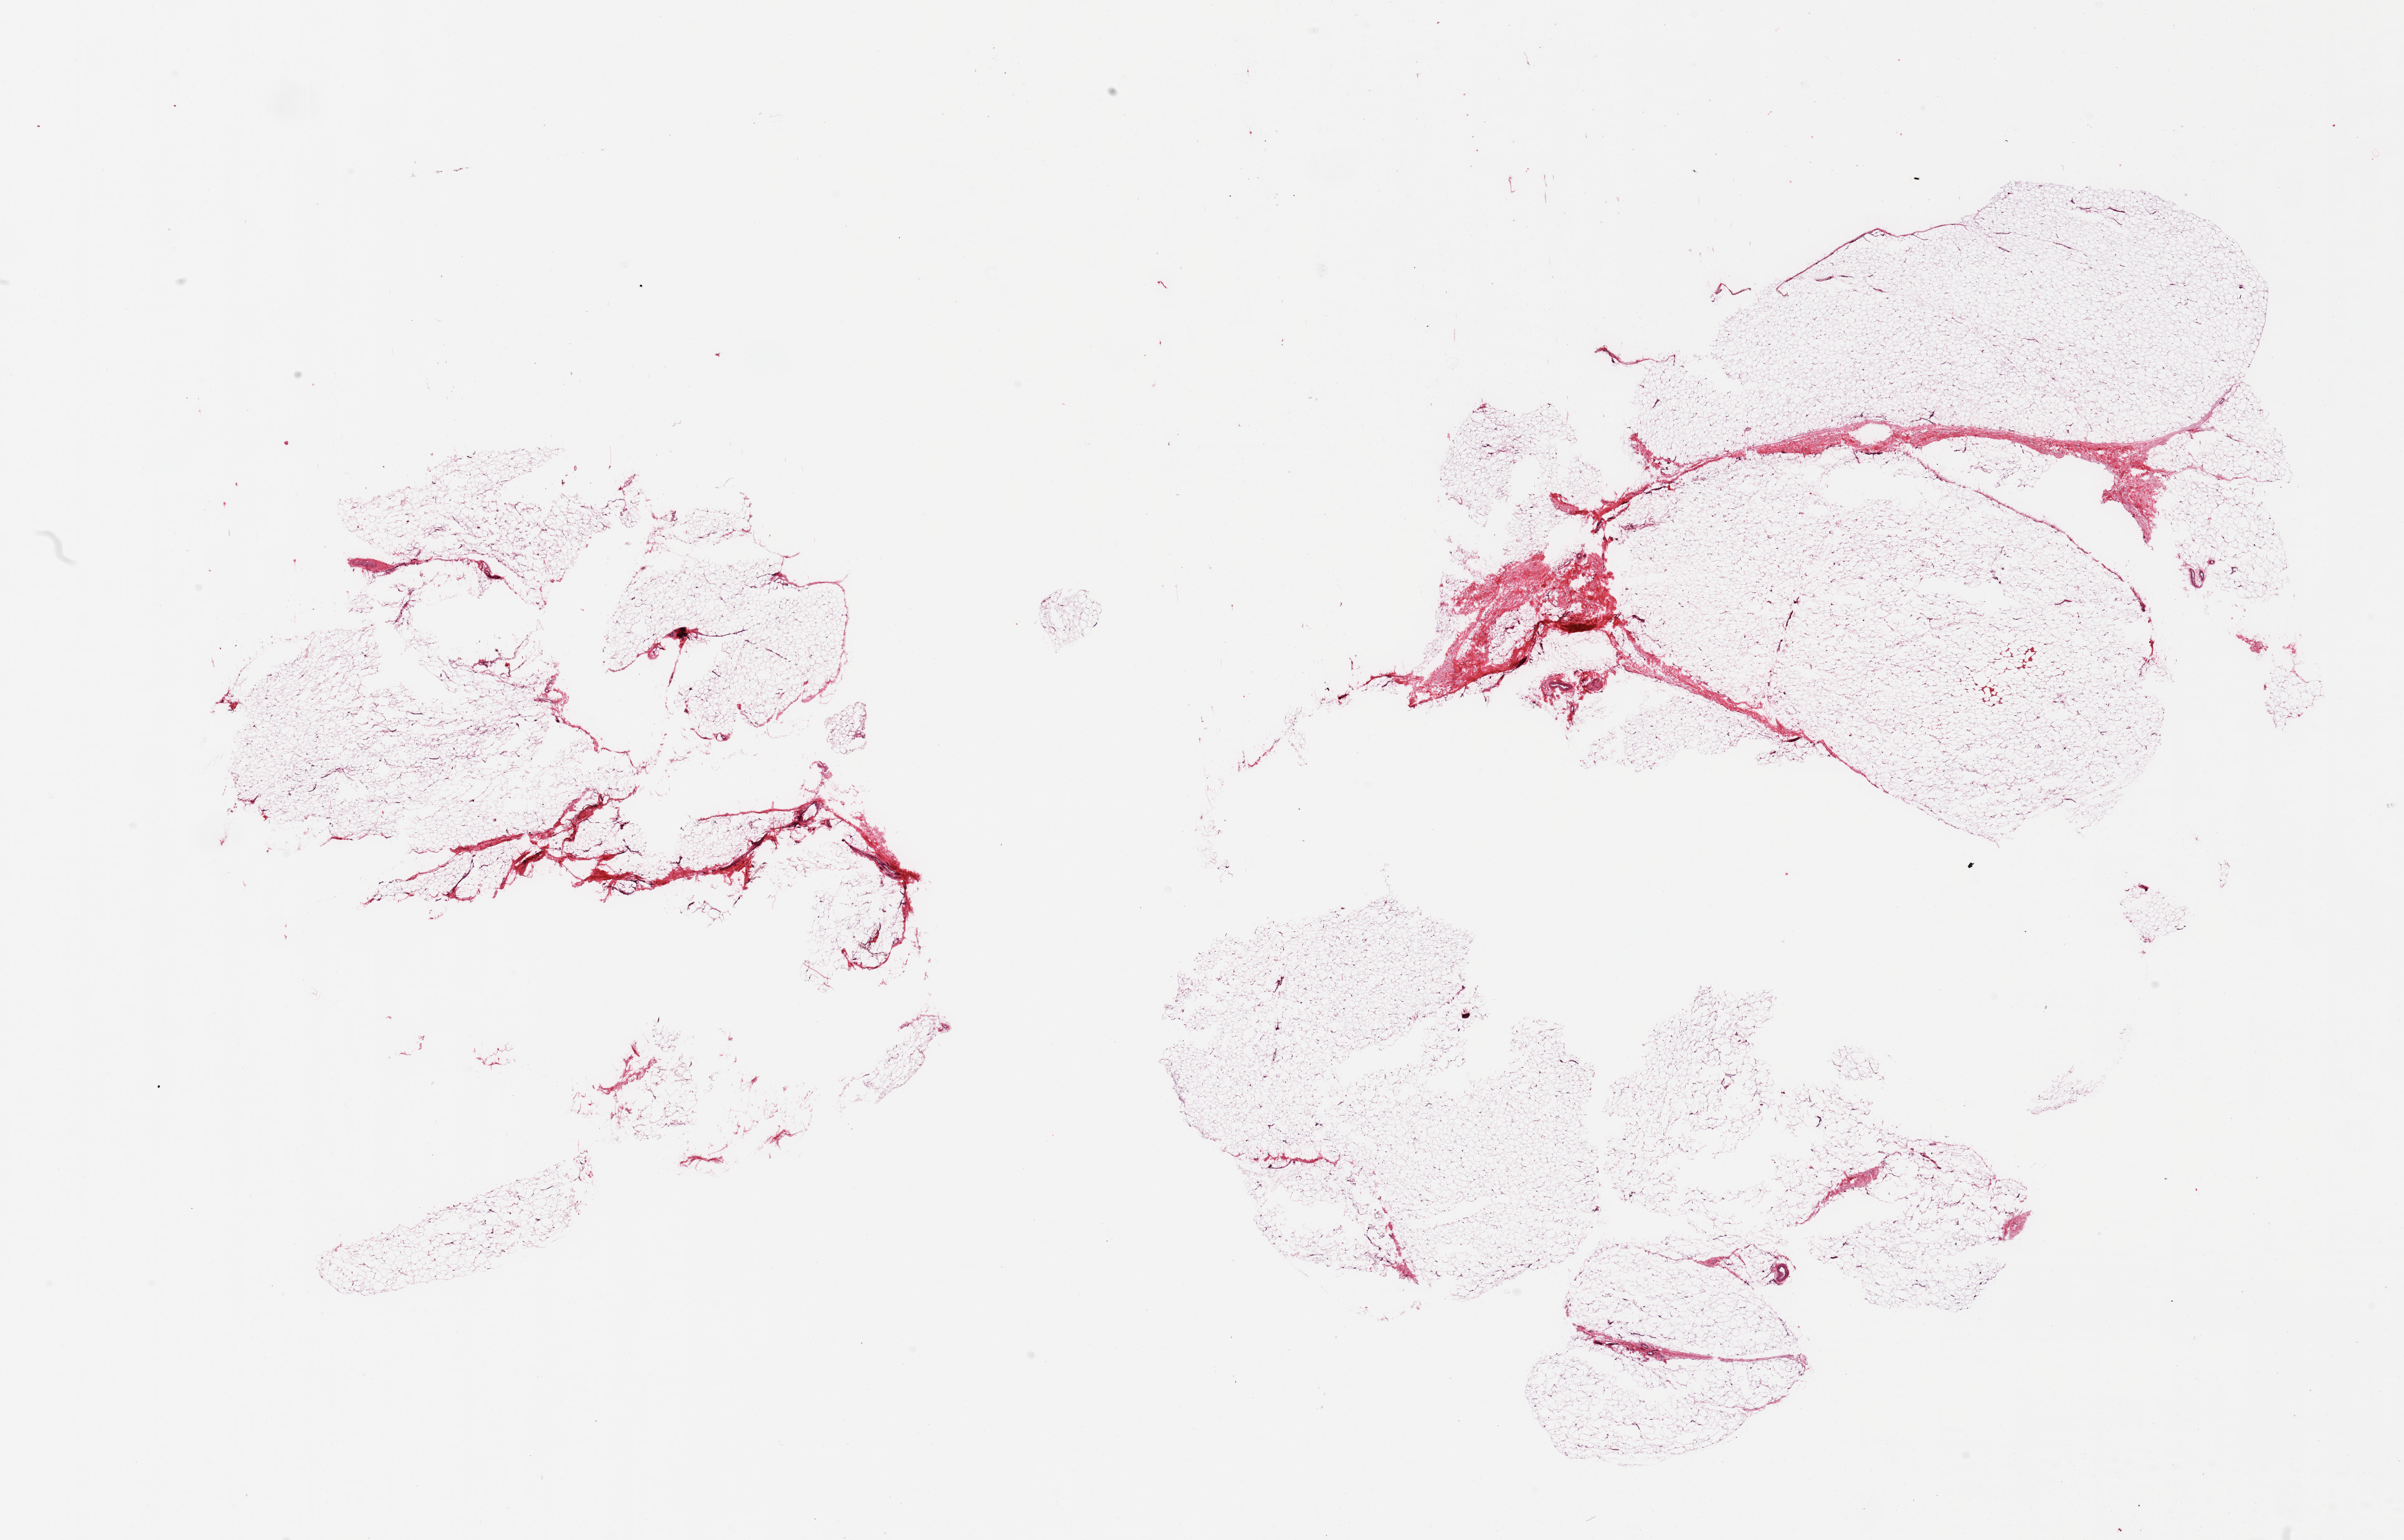
Digitized hematoxylin and eosin (H&E)-stained section, low-resolution overview of the scanned area, about 30.5 x 19.5 mm, PAXgene-fixed paraffin-embedded (PFPE) section, section of adipose tissue (target tissue), donor tissue sample. Female donor.
Pathologist's review note for this sample: 2 fragmented pieces; mature adipose tissue and 5% and 10% fibrovascular component.